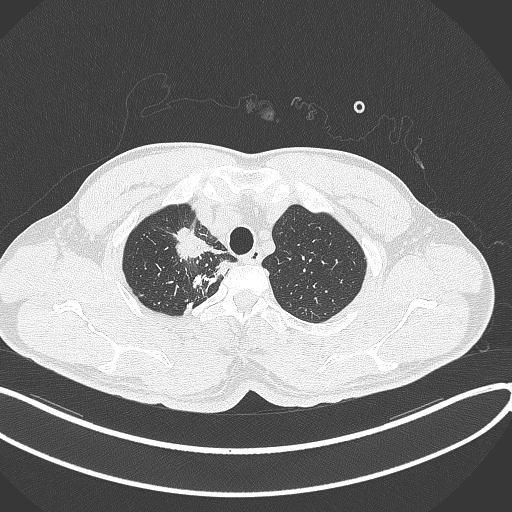
Chest CT, one axial slice; slice 326 of 391 in the series (ordered by position); reconstruction kernel B70f; 120 kVp; lung window (W 1500 / L -600 HU); 1 mm slice thickness; 512 × 512 image matrix. Patient: male, 48 years. From the clinical record (not read from this slice): clinical TNM (as recorded): T1c N1 M1.
Structures marked on this image (rectangle marked by the reading radiologist):
- lung tumour (recorded histology: adenocarcinoma): box from (x=167, y=222) to (x=208, y=261) px